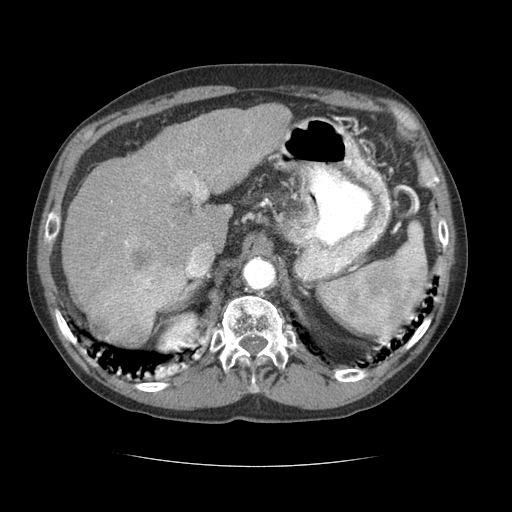
Contrast-enhanced abdominal CT (liver protocol), one axial slice. Reconstruction kernel STANDARD. 120 kVp. Soft-tissue window (W 400 / L 40 HU). 2.5 mm slice thickness. 512 × 512 image matrix, field of view 360 × 360 mm. Case-level facts recorded for this patient, not image findings: diagnosis: hepatocellular carcinoma (patient treated with transarterial chemoembolisation; whether this scan precedes or follows treatment is not stated here); TNM stage (as recorded): Stage-II; Child-Pugh class: B; tumour differentiation: poorly differentiated.
Outlined on this slice (semi-automatically segmented with operator editing):
- liver parenchyma outside the tumour (the mass and vessels are separate outlines, so this box may not span the whole liver): bounding box (x1, y1, x2, y2) in pixels: (62, 104, 292, 342)
- mass: (99, 233, 186, 347)
- liver vessels: (171, 171, 209, 256)